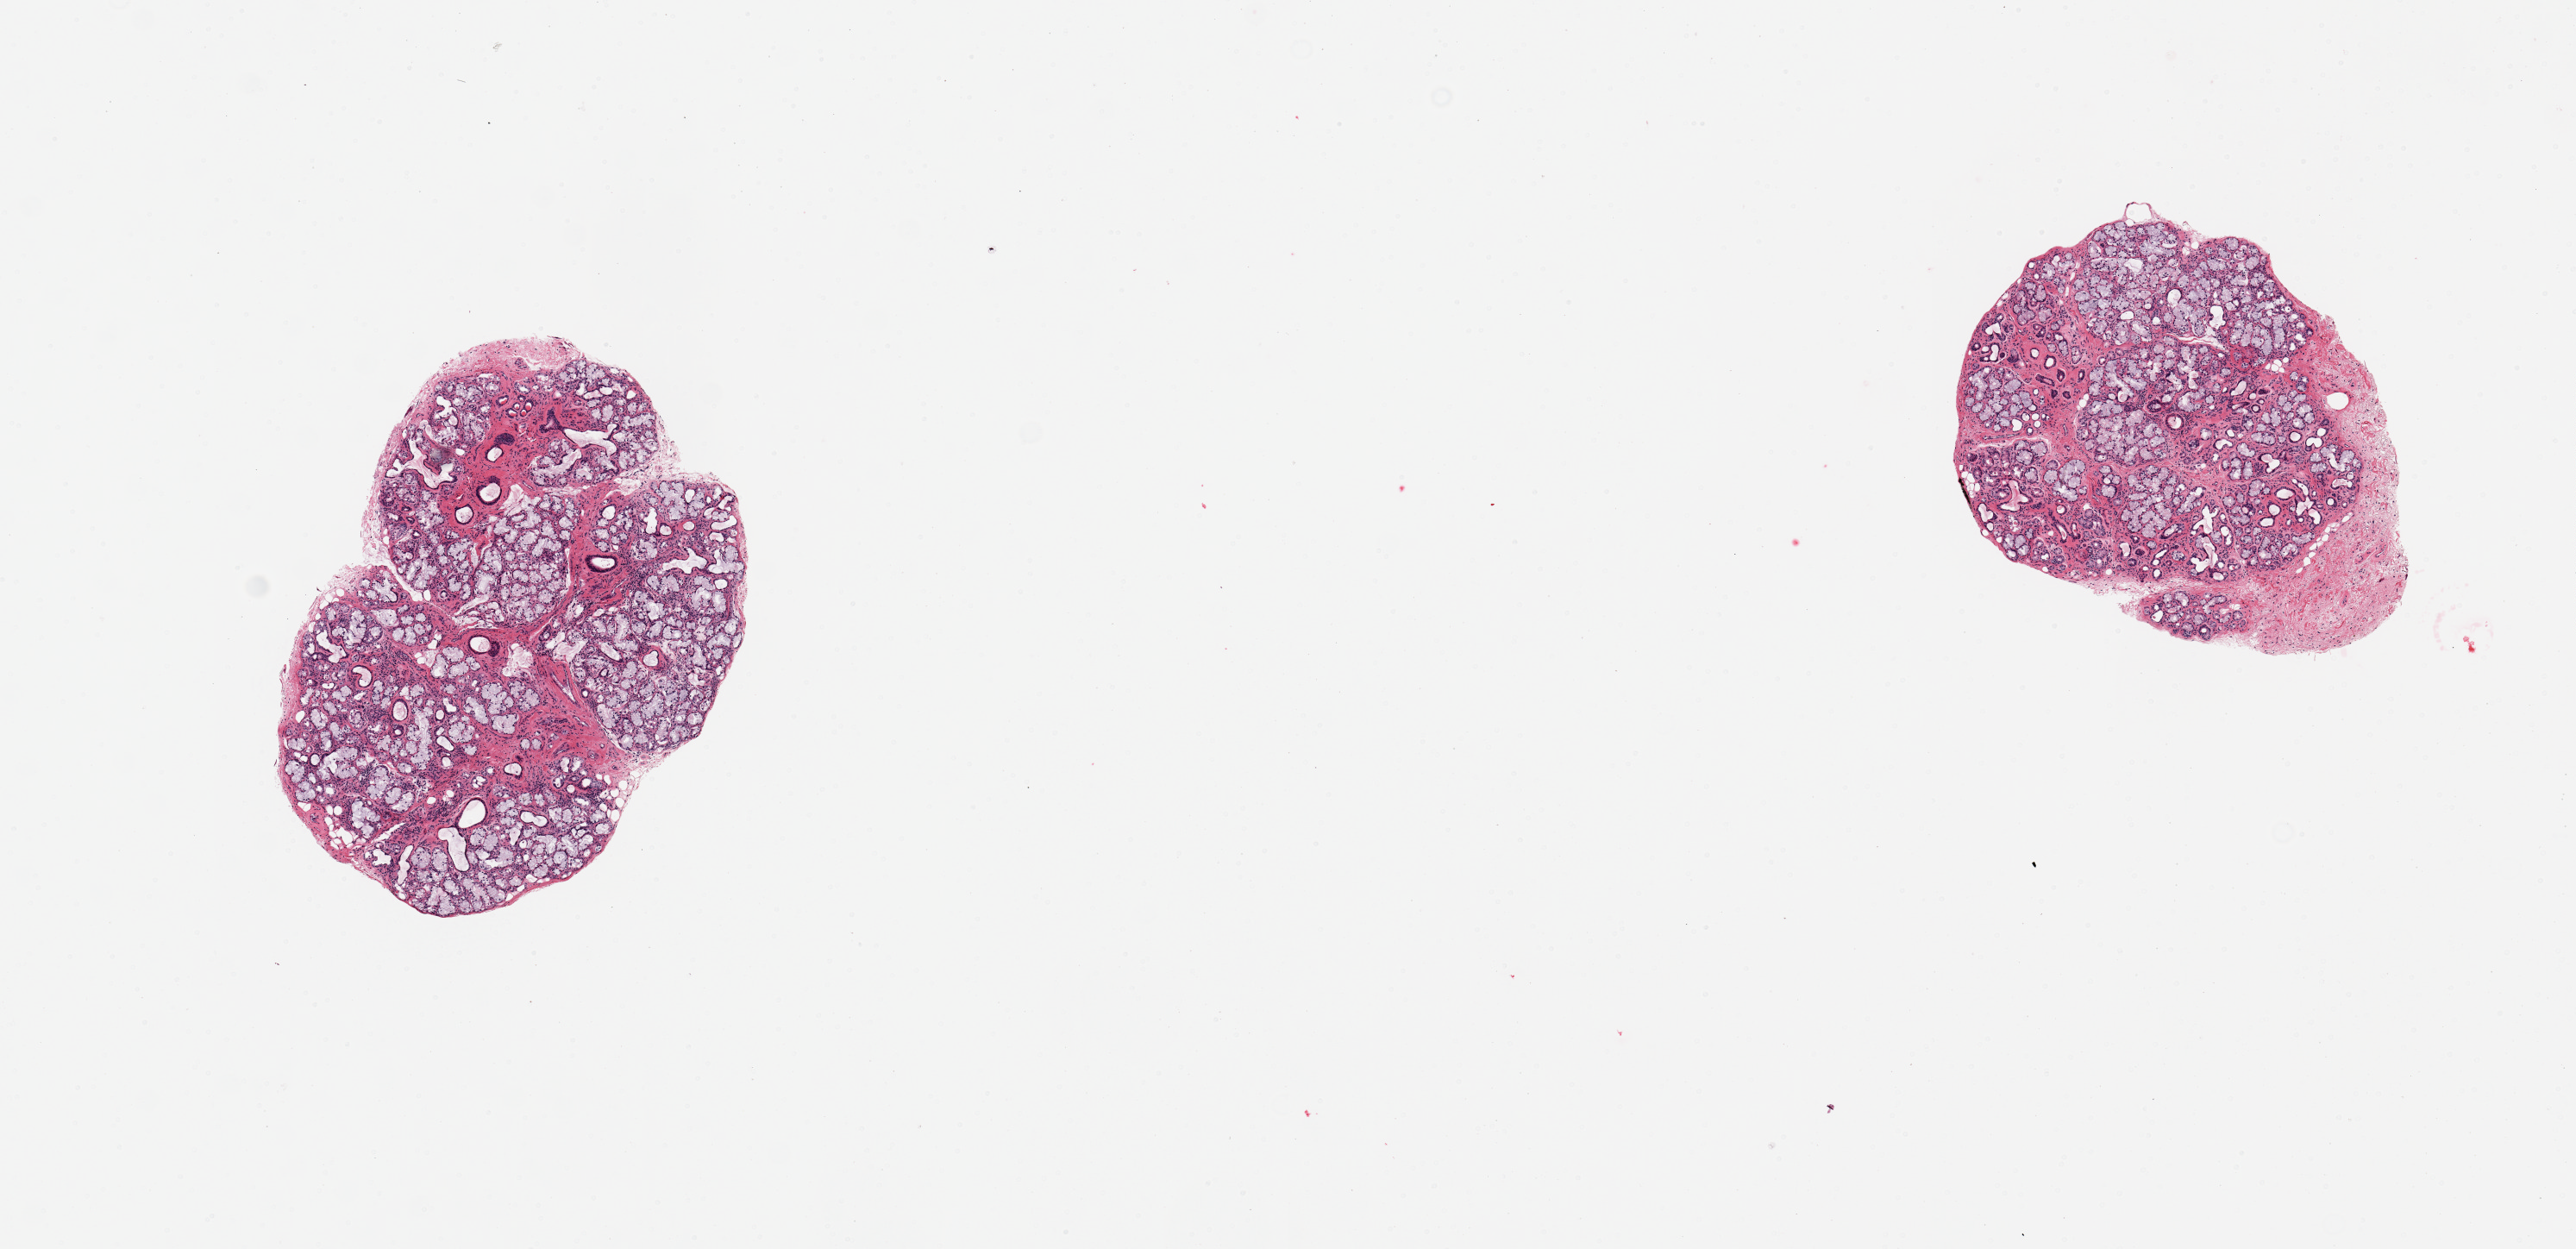
Hematoxylin and eosin (H&E) whole-slide image, brightfield, low-resolution overview of the scanned area, about 11.8 x 5.7 mm (slide scanned at 20x); PAXgene-fixed paraffin-embedded (PFPE) section; sampled site (target tissue): minor salivary gland; tissue donor sample.
- review note (as recorded): 2 pieces, 90% glandular elements, good specimens; ~10% stroma